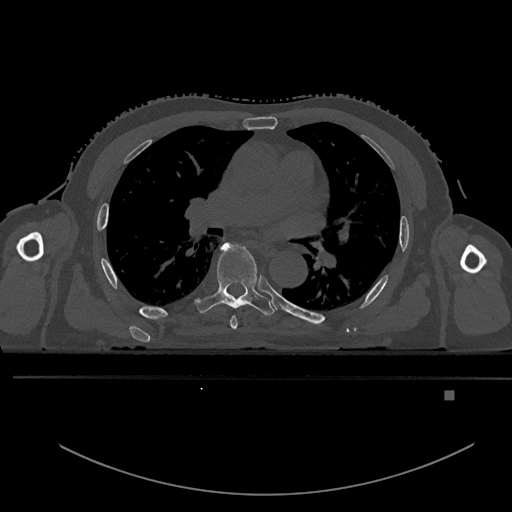
CT including the spine, one axial slice. Bone window (W 1800 / L 400 HU). 0.5 mm slice thickness. 512 × 512 image matrix. Male patient, age 82 years. From the clinical record (not read from this slice): primary cancer: prostate; vertebrae with lytic lesions (as recorded): T11, T9, T8, T2.
Structures marked on this image (semi-automatic segmentation, software-assisted and operator-edited):
- T5 vertebra: box from (x=230, y=315) to (x=238, y=330) px
- T6 vertebra: (x=195, y=242)–(x=276, y=316)